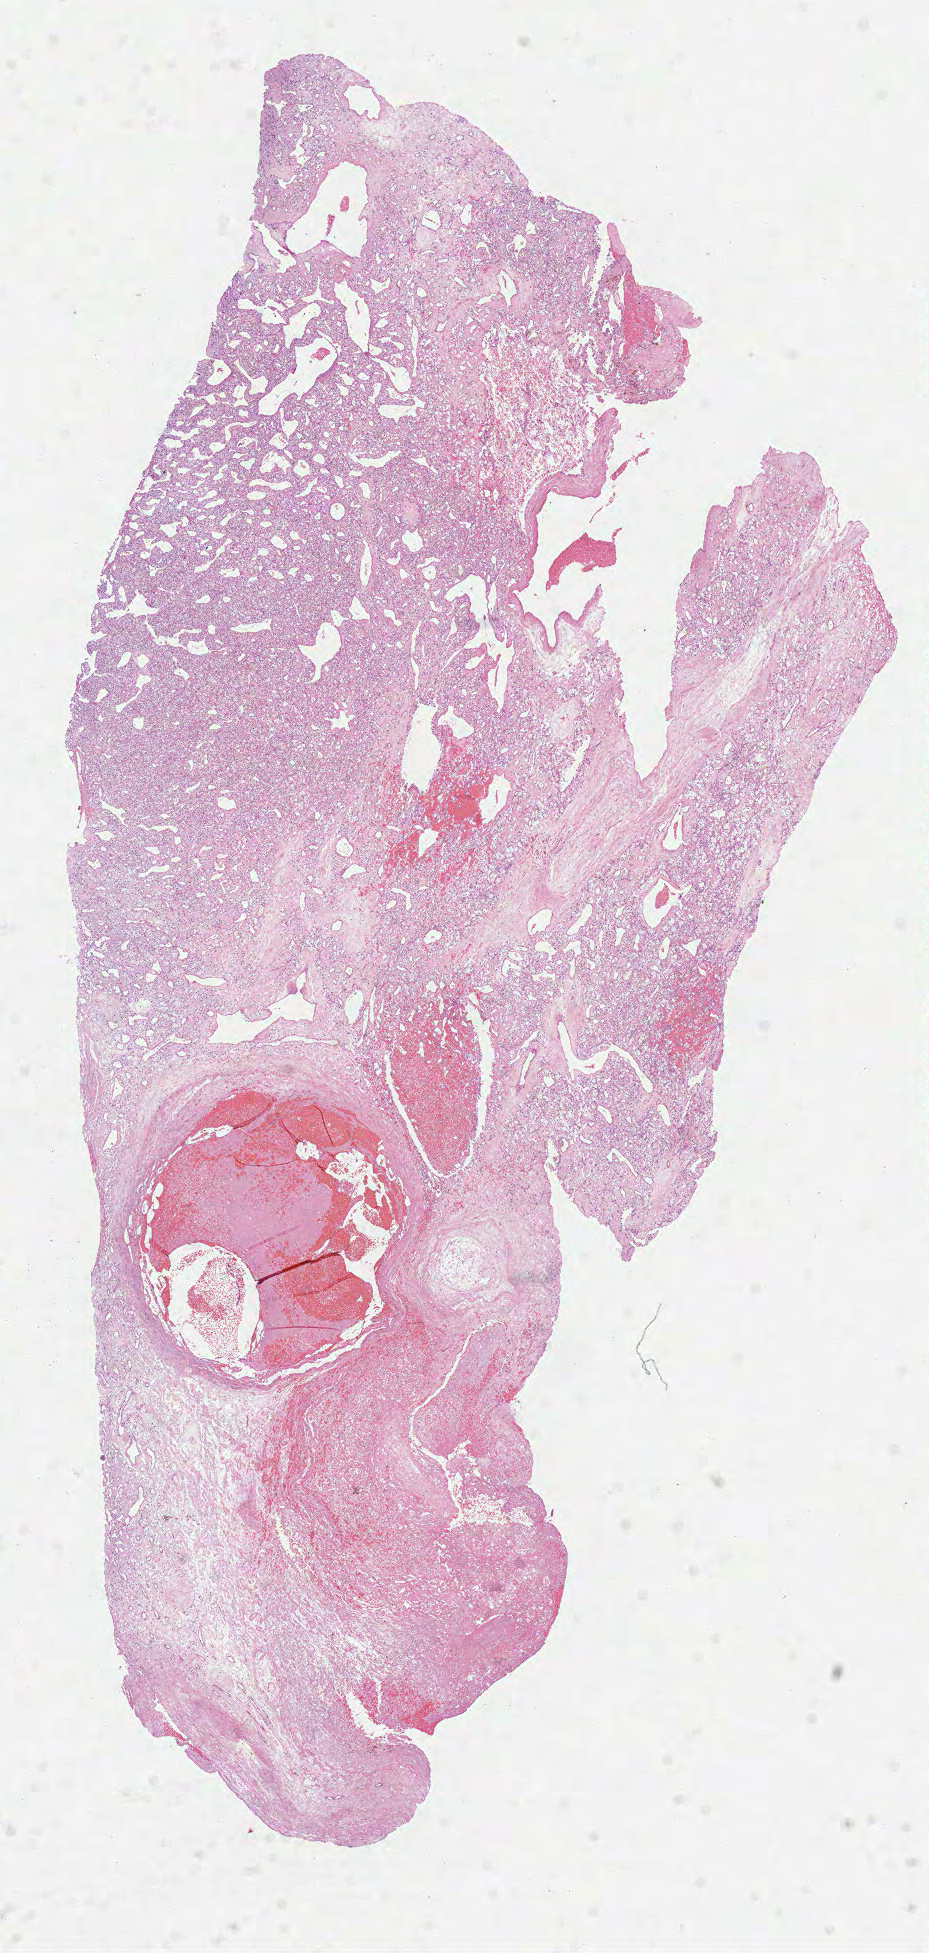
Digitized Hematoxylin and eosin (H&E) stained tissue section (whole slide) — whole scanned area (about 7.5 x 15.8 mm) shown as a low-resolution overview. Formalin-fixed paraffin-embedded (FFPE) diagnostic section. Primary tumour sample from the kidney. Patient: male, age at initial diagnosis 74 years.
Diagnosis: Clear cell adenocarcinoma, NOS.